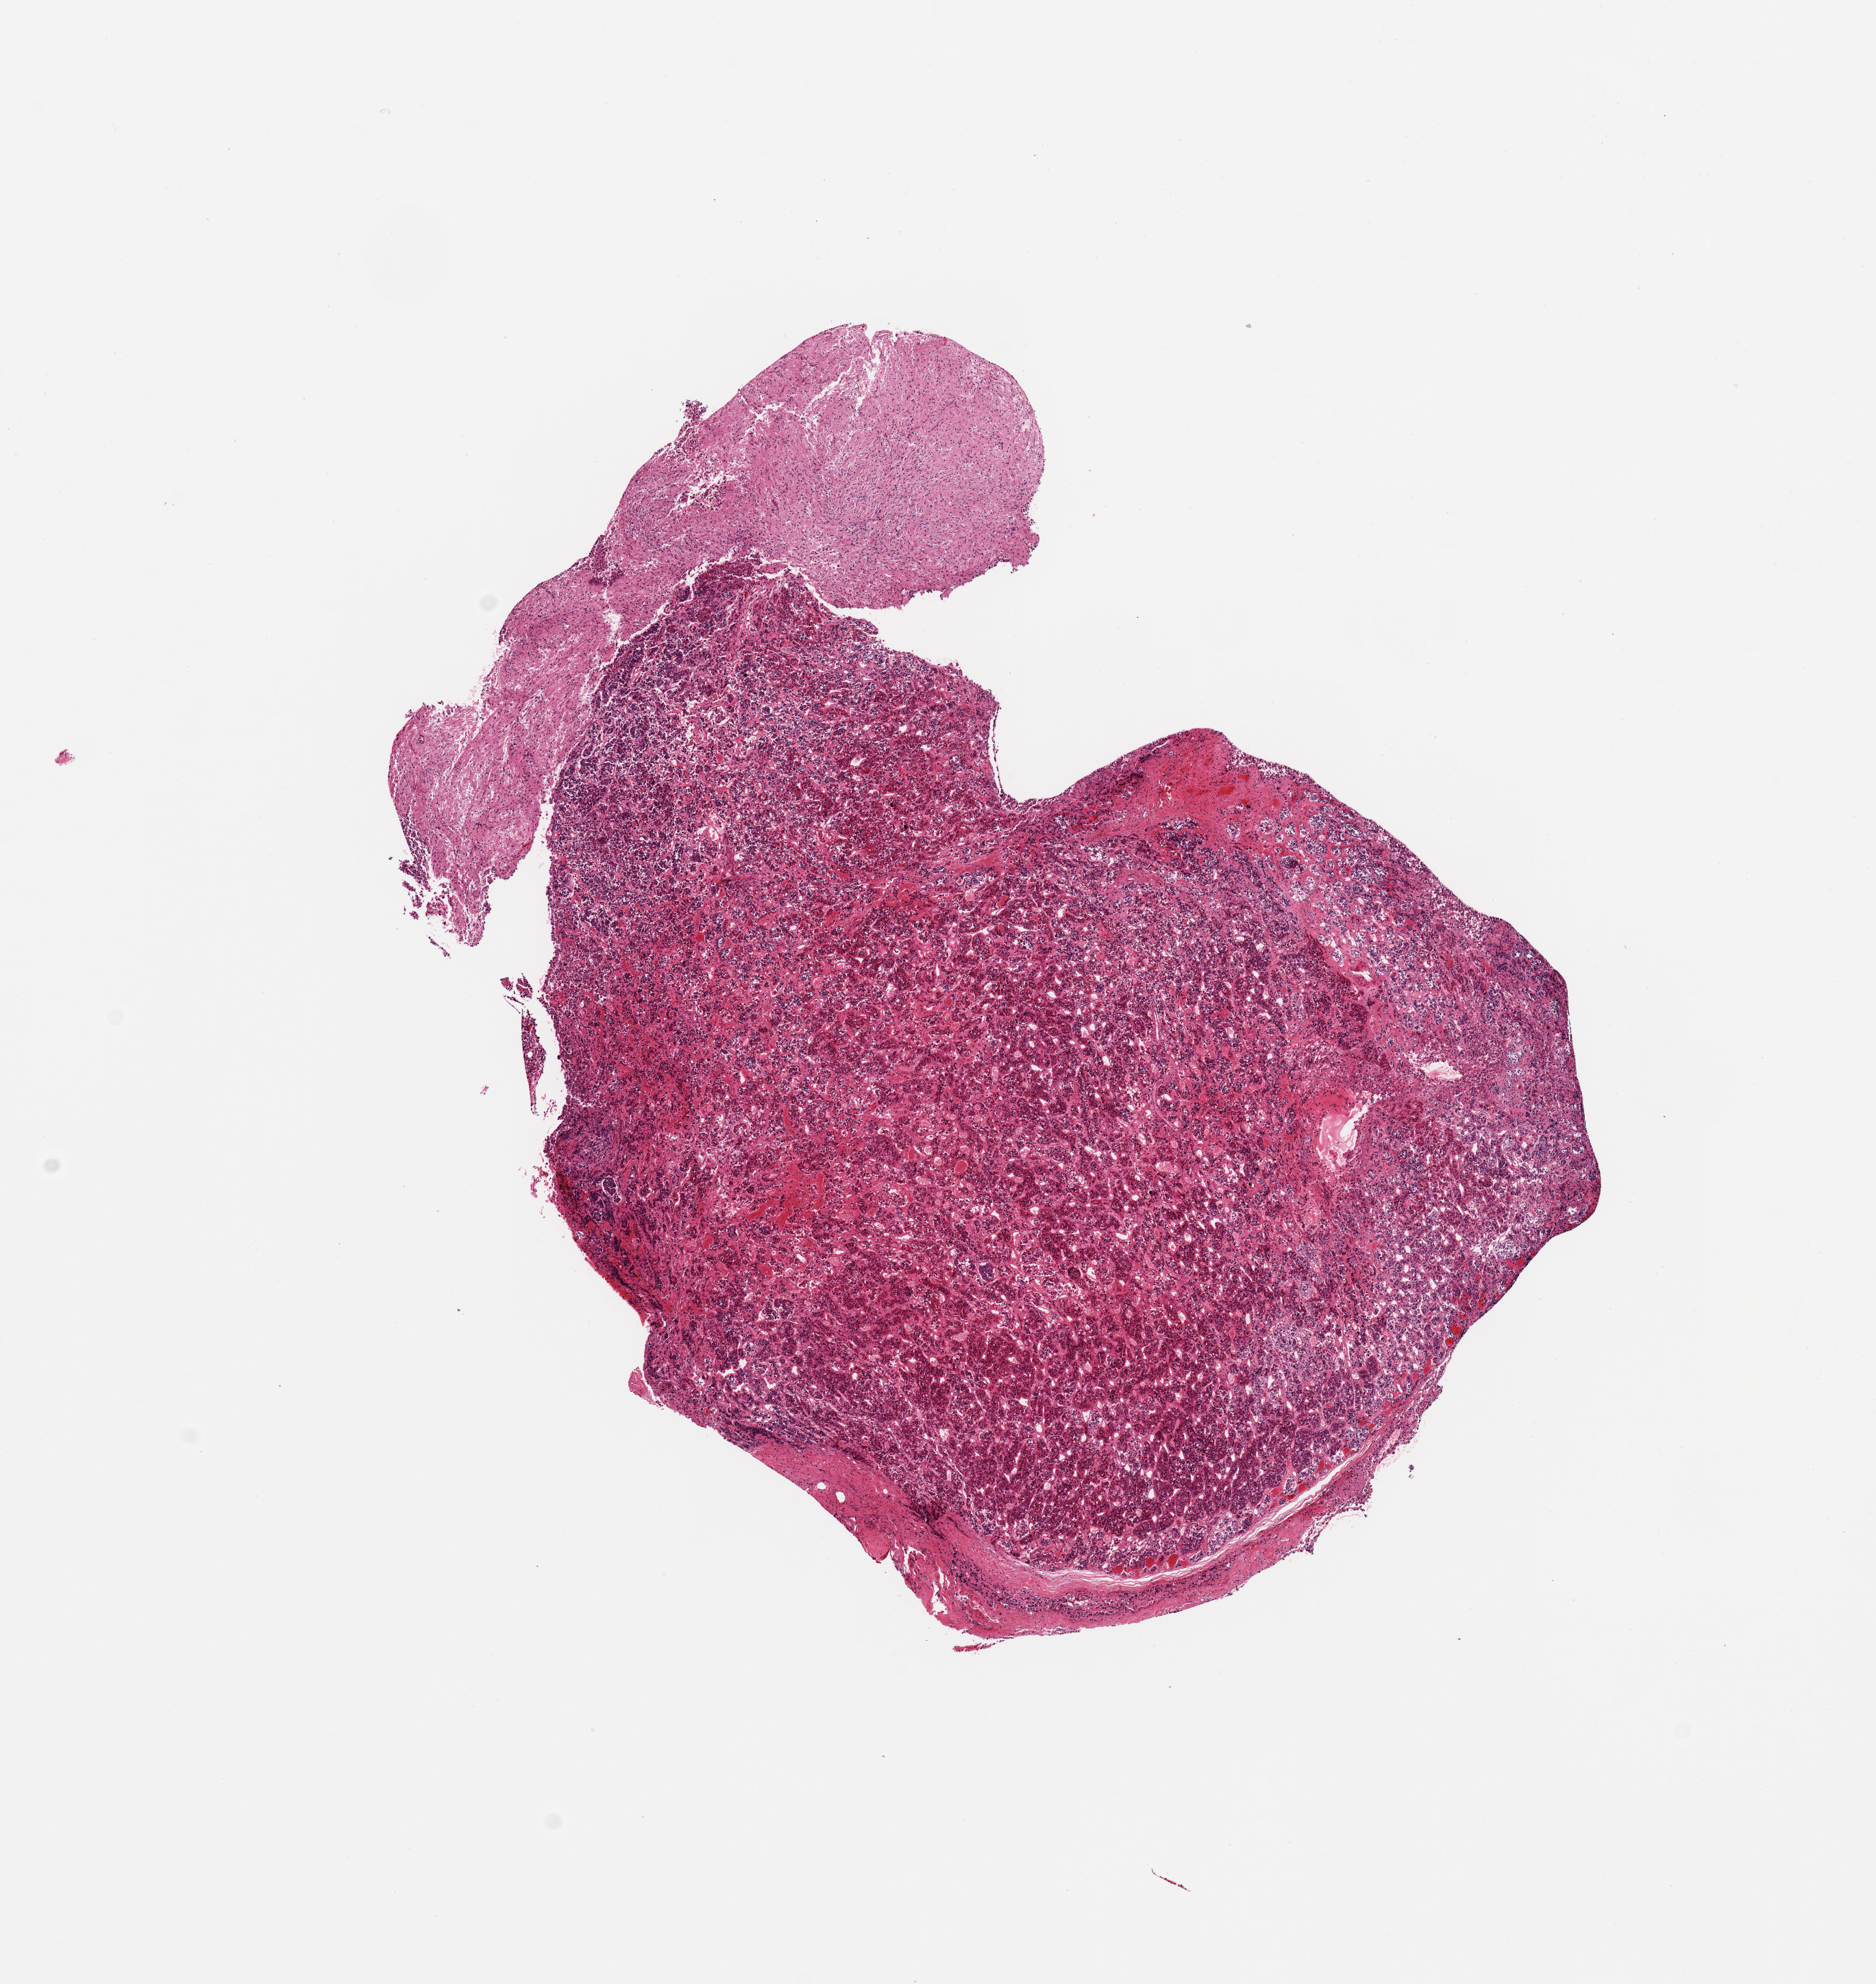
Hematoxylin and eosin (H&E) whole-slide image, low-resolution overview of the scanned area, about 10.8 x 11.5 mm. PAXgene-fixed, paraffin-embedded tissue. Section of pituitary (target tissue). Donor tissue sample.
Pathologist's review note for this sample: 1 piece, adenohypophysis; ~4x1.5mm nubbin of neurohypophysis is ~10% of tissue.